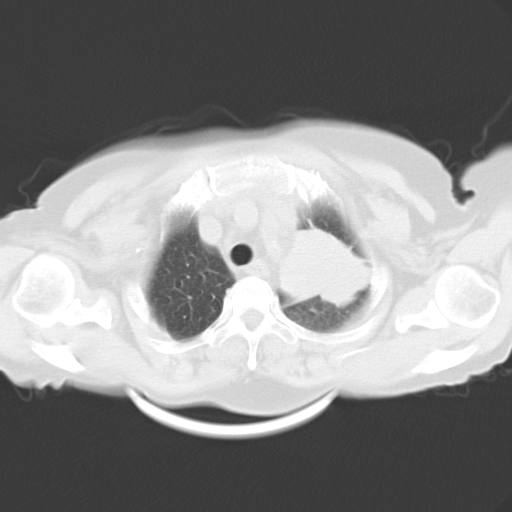
Chest CT, one axial slice. Slice 23 of 26 in the series (ordered by position). Reconstruction kernel B40f. 120 kVp. Lung window (W 1500 / L -600 HU). 512 × 512 image matrix, field of view 353 × 353 mm. Patient: female, 71 years. From the clinical record (not read from this slice): clinical TNM (as recorded): T3 N3 M0.
Outlined on this slice (rectangle marked by the reading radiologist):
- lung tumour (recorded histology: adenocarcinoma): box from (x=272, y=213) to (x=382, y=327) px